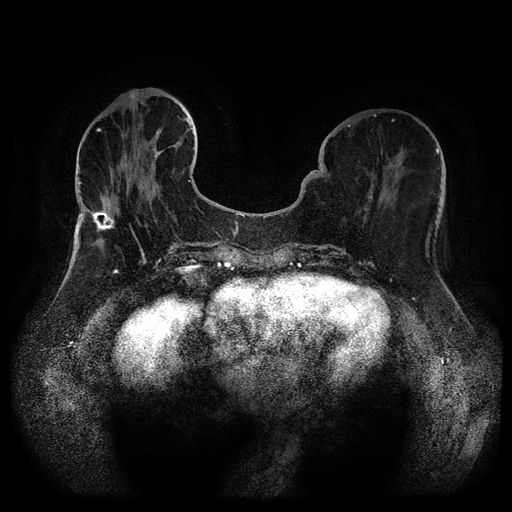
Breast MRI (dynamic contrast-enhanced, multi-phase), one axial slice; slice 35 of 116 in the series (ordered by position); dynamic contrast-enhanced series, time point 2 of 5 at this slice position (early post-contrast); 1.5 T; TE 2.6 ms, TR 5.3 ms; 512 × 512 image matrix, field of view 350 × 350 mm. Female patient, age 75 years.
Annotated regions visible in this slice (semi-automatically segmented with operator editing):
- breast lesion (labelled benign in the annotation): box from (x=89, y=207) to (x=117, y=234) px